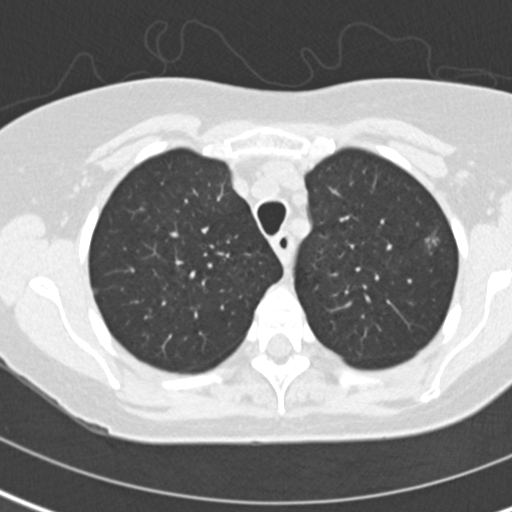
Low-dose screening chest CT, one axial slice. Position 112 of 141 along the scan axis. Lung window (W 1500 / L -600 HU). 512 × 512 image matrix.
Outlined on this slice (outlined manually by an expert reader):
- lesion 1 (tumor, upper lobe of left lung): box from (x=425, y=238) to (x=438, y=248) px